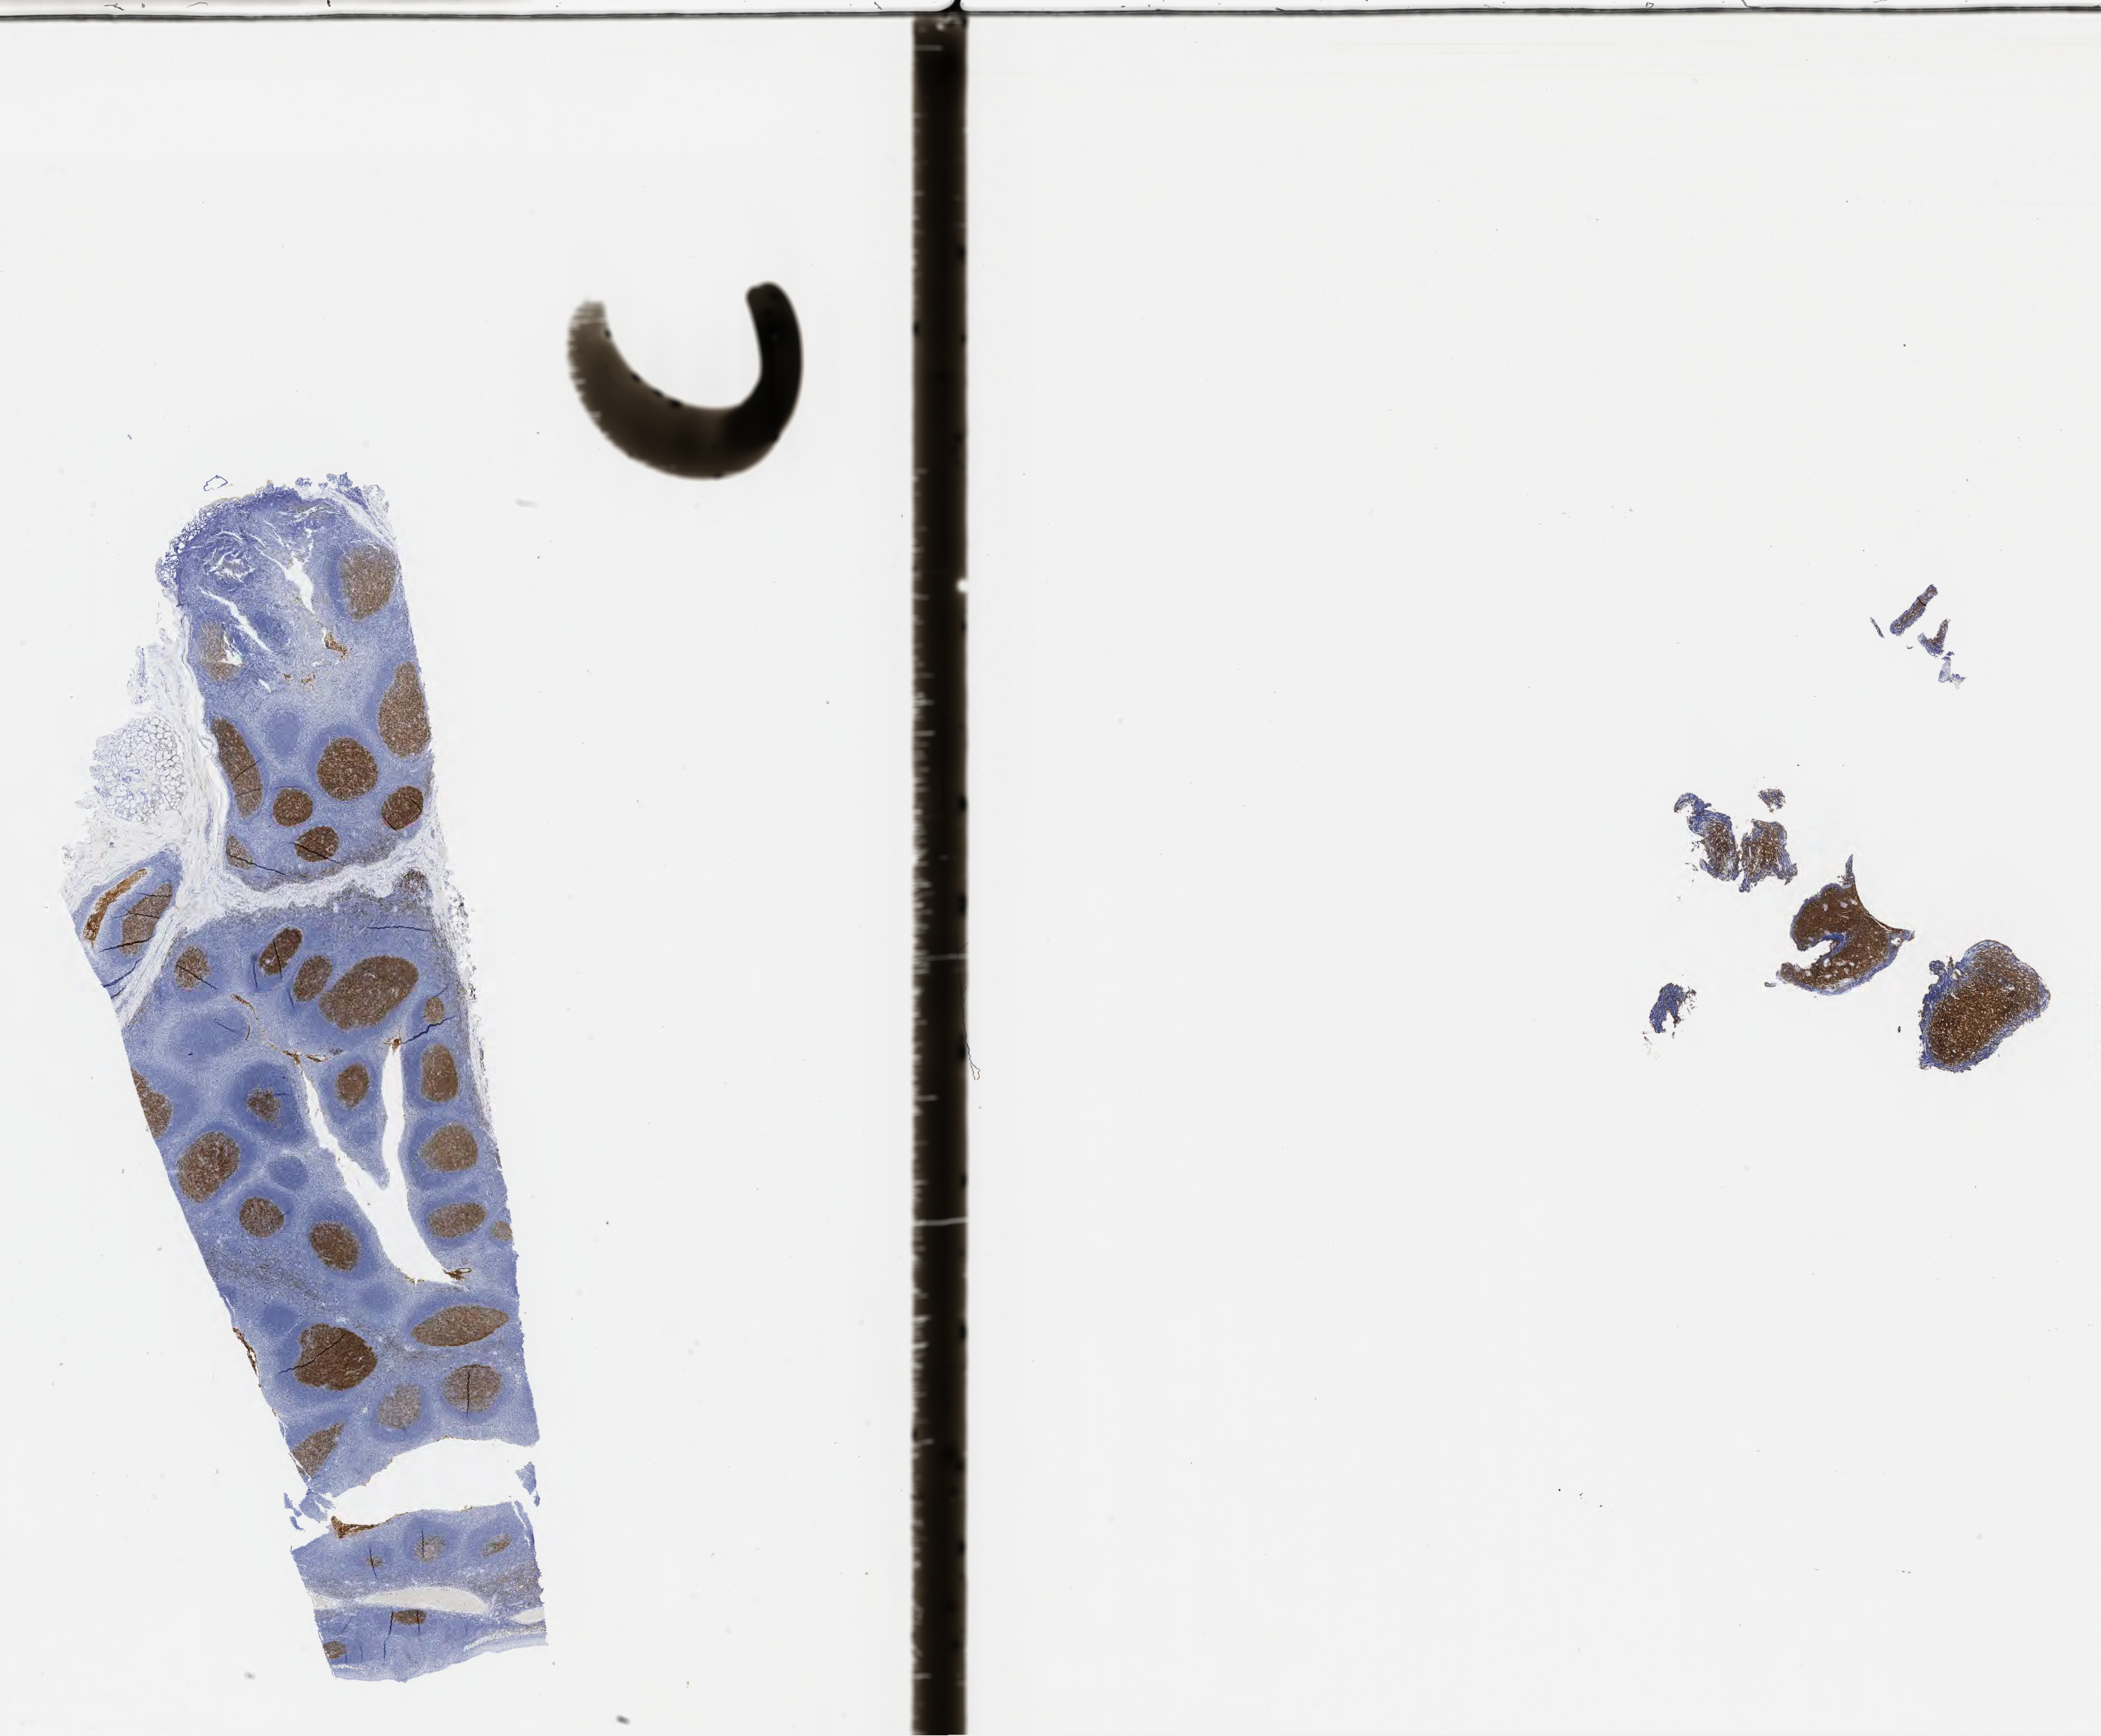
Whole-slide image, immunohistochemical stain for CD10 — shown as a low-resolution overview of the whole scanned area (about 24.7 x 20.4 mm), tumor tissue, anatomic site: small intestine. Patient female; 47 years old.
• histologic diagnosis: Burkitt lymphoma, NOS